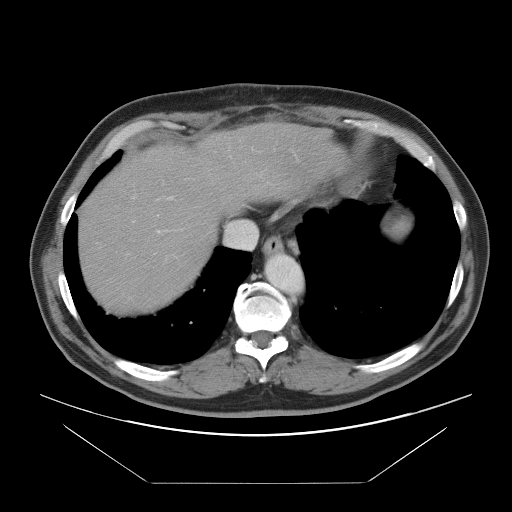
Contrast-enhanced abdominal CT, one axial slice; position 80 of 97 along the scan axis; 120 kVp; intravenous contrast given; soft-tissue window (W 400 / L 40 HU); 5 mm slice thickness; 512 × 512 image matrix, field of view 442 × 442 mm. Male patient, age 62 years. From the clinical record (not read from this slice): diagnosis: colorectal cancer liver metastases, imaged before liver resection; multiple liver metastases: no; largest metastasis: 7 cm; disease in both lobes: yes.
Annotated regions visible in this slice (manually delineated by an expert):
- hepatic veins: bounding box [x1, y1, x2, y2] px = [225, 220, 258, 249]
- liver: [79, 126, 331, 312]
- planned liver remnant (the part of the liver to remain after resection): [80, 176, 219, 312]
- portal vein (with intrahepatic branches): [133, 197, 173, 233]